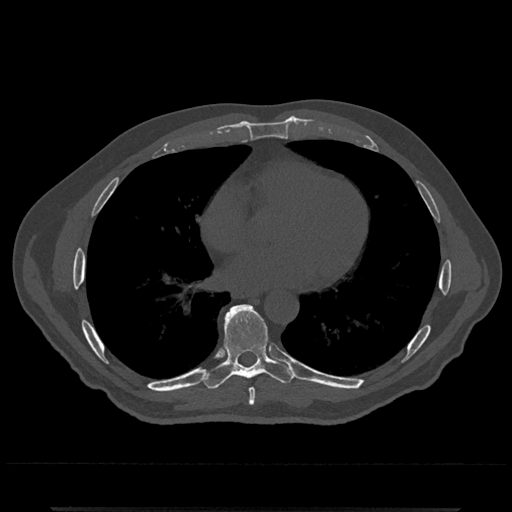
CT including the spine, one axial slice. Slice 678 of 797 in the series (ordered by position). 120 kVp. Bone window (W 1800 / L 400 HU). 0.5 mm slice thickness. 512 × 512 image matrix, field of view 393 × 393 mm. Patient: male, 67 years. From the clinical record (not read from this slice): primary cancer: prostate.
Outlined on this slice (semi-automatically segmented with operator editing):
- T7 vertebra: box from (x=248, y=388) to (x=256, y=406) px
- T8 vertebra: (x=202, y=305)–(x=295, y=390)